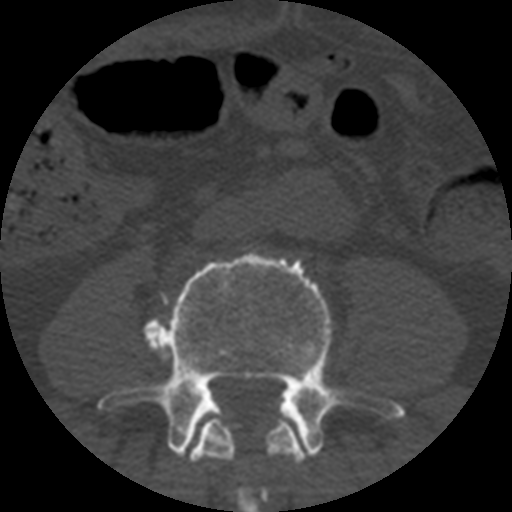
CT including the spine, one axial slice. Slice 99 of 508 in the series (ordered by position). Reconstruction kernel STANDARD. 120 kVp. Bone window (W 1800 / L 400 HU). 1.25 mm slice thickness. 512 × 512 image matrix. Patient age 57 years. Case-level facts recorded for this patient, not image findings: primary cancer: prostate.
Structures marked on this image (semi-automatically segmented with operator editing):
- L3 vertebra: bounding box <189,416,306,512> (left, top, right, bottom; pixels)
- L4 vertebra: <98,251,405,457>